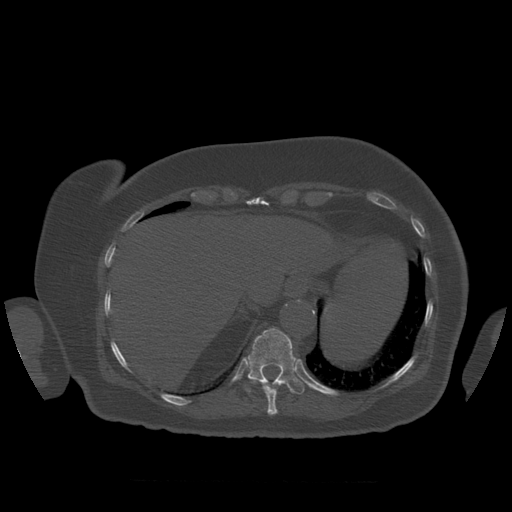
CT including the spine, one axial slice; position 328 of 399 along the scan axis; reconstruction kernel STANDARD; 120 kVp; bone window (W 1800 / L 400 HU); 512 × 512 image matrix. Patient age 81 years. From the clinical record (not read from this slice): primary cancer: renal; vertebrae with lytic lesions (as recorded): L1.
Annotated regions visible in this slice (semi-automatically segmented with operator editing):
- T10 vertebra: bounding box [x1, y1, x2, y2] px = [263, 386, 278, 416]
- T11 vertebra: [247, 328, 304, 395]